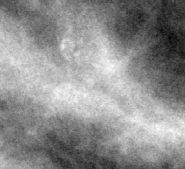
Region of interest cut from a scanned film mammogram (one marked finding); left breast; MLO view; BI-RADS breast density category 2 (scale 1–4).
- Marked abnormality: calcifications, morphology pleomorphic, distribution clustered; BI-RADS assessment category 4; subtlety rating 2 on a 1 (subtle) to 5 (obvious) scale; pathology result (as recorded, not read from the image): benign.